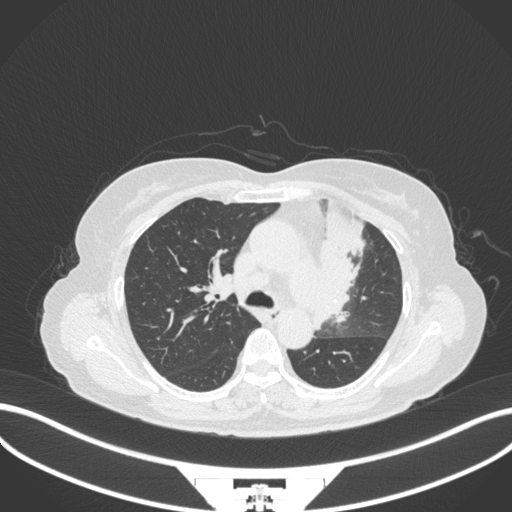
Chest CT, one axial slice; slice 222 of 382 in the series (ordered by position); lung window (W 1500 / L -600 HU); 1 mm slice thickness; 512 × 512 image matrix, field of view 400 × 400 mm. Patient: female, 64 years. Case-level facts recorded for this patient, not image findings: clinical TNM (as recorded): T2a N2 M0.
Structures marked on this image (bounding box drawn by a radiologist):
- lung tumour (recorded histology: adenocarcinoma): bounding box <312,196,369,332> (left, top, right, bottom; pixels)